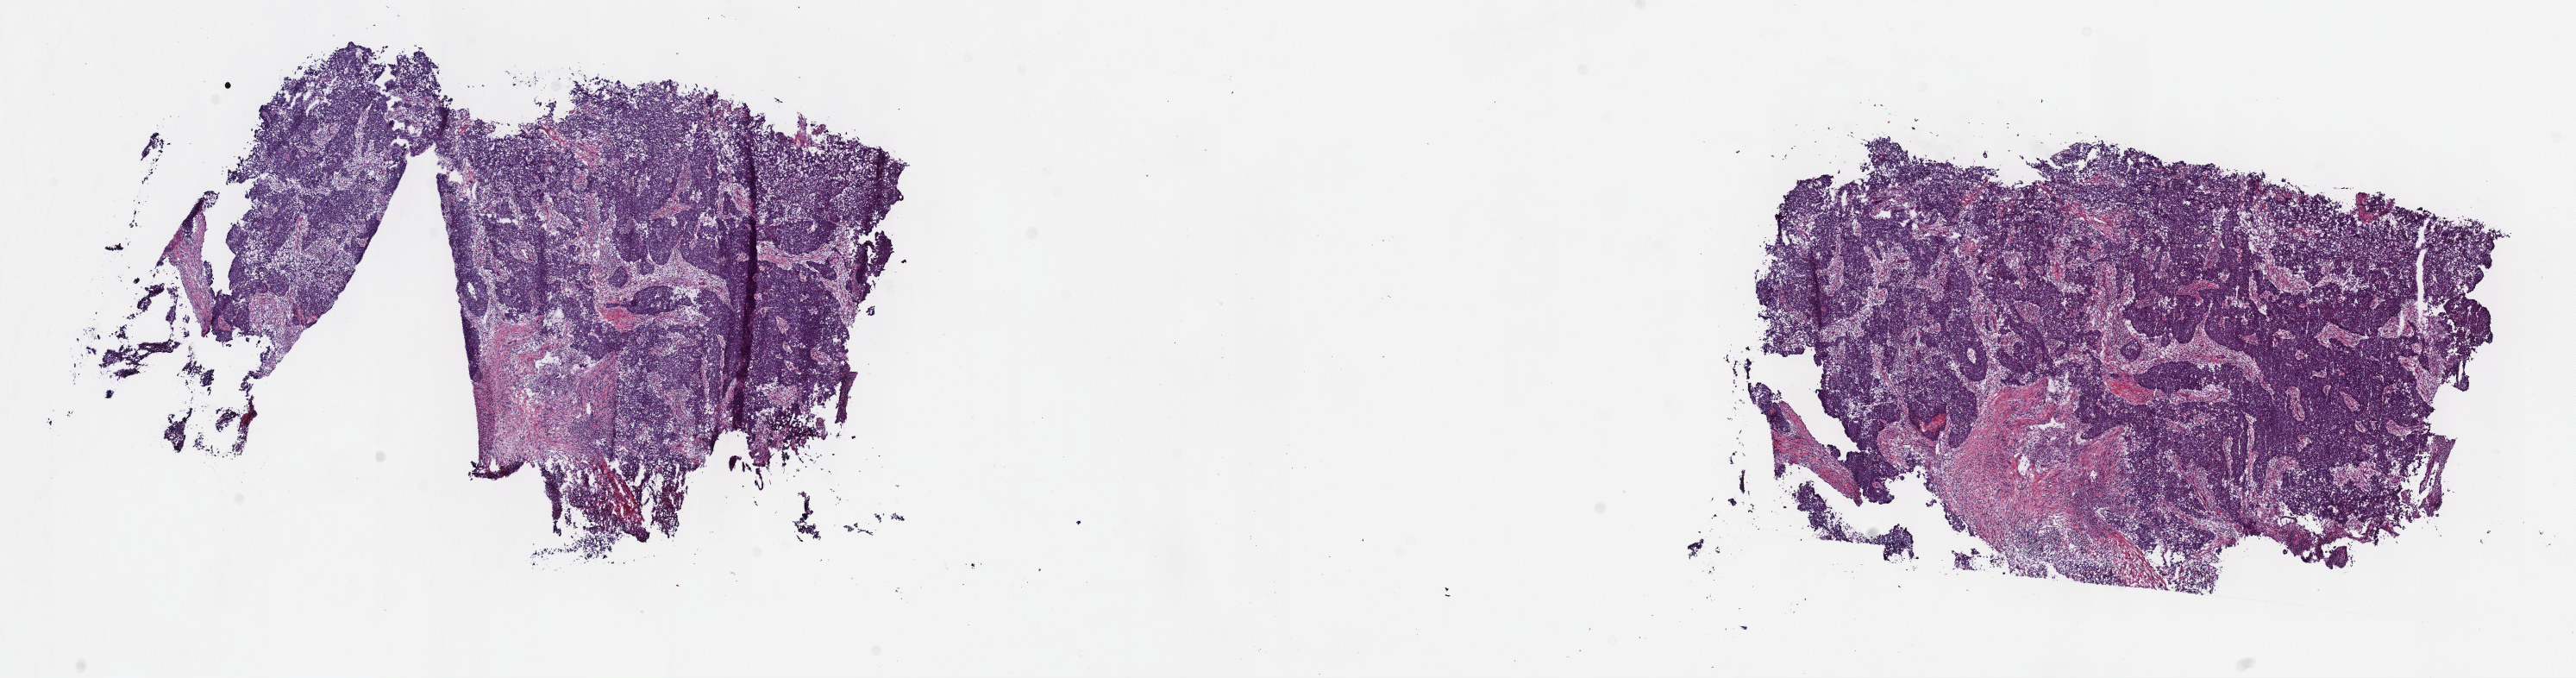
Whole-slide histology image, H&E — low-resolution overview of the scanned area, about 24.2 x 6.4 mm (slide scanned at 40x), frozen section, thymus, primary tumour sample. Patient: male, age at initial diagnosis 63 years.
Diagnosis: Thymic carcinoma, NOS.